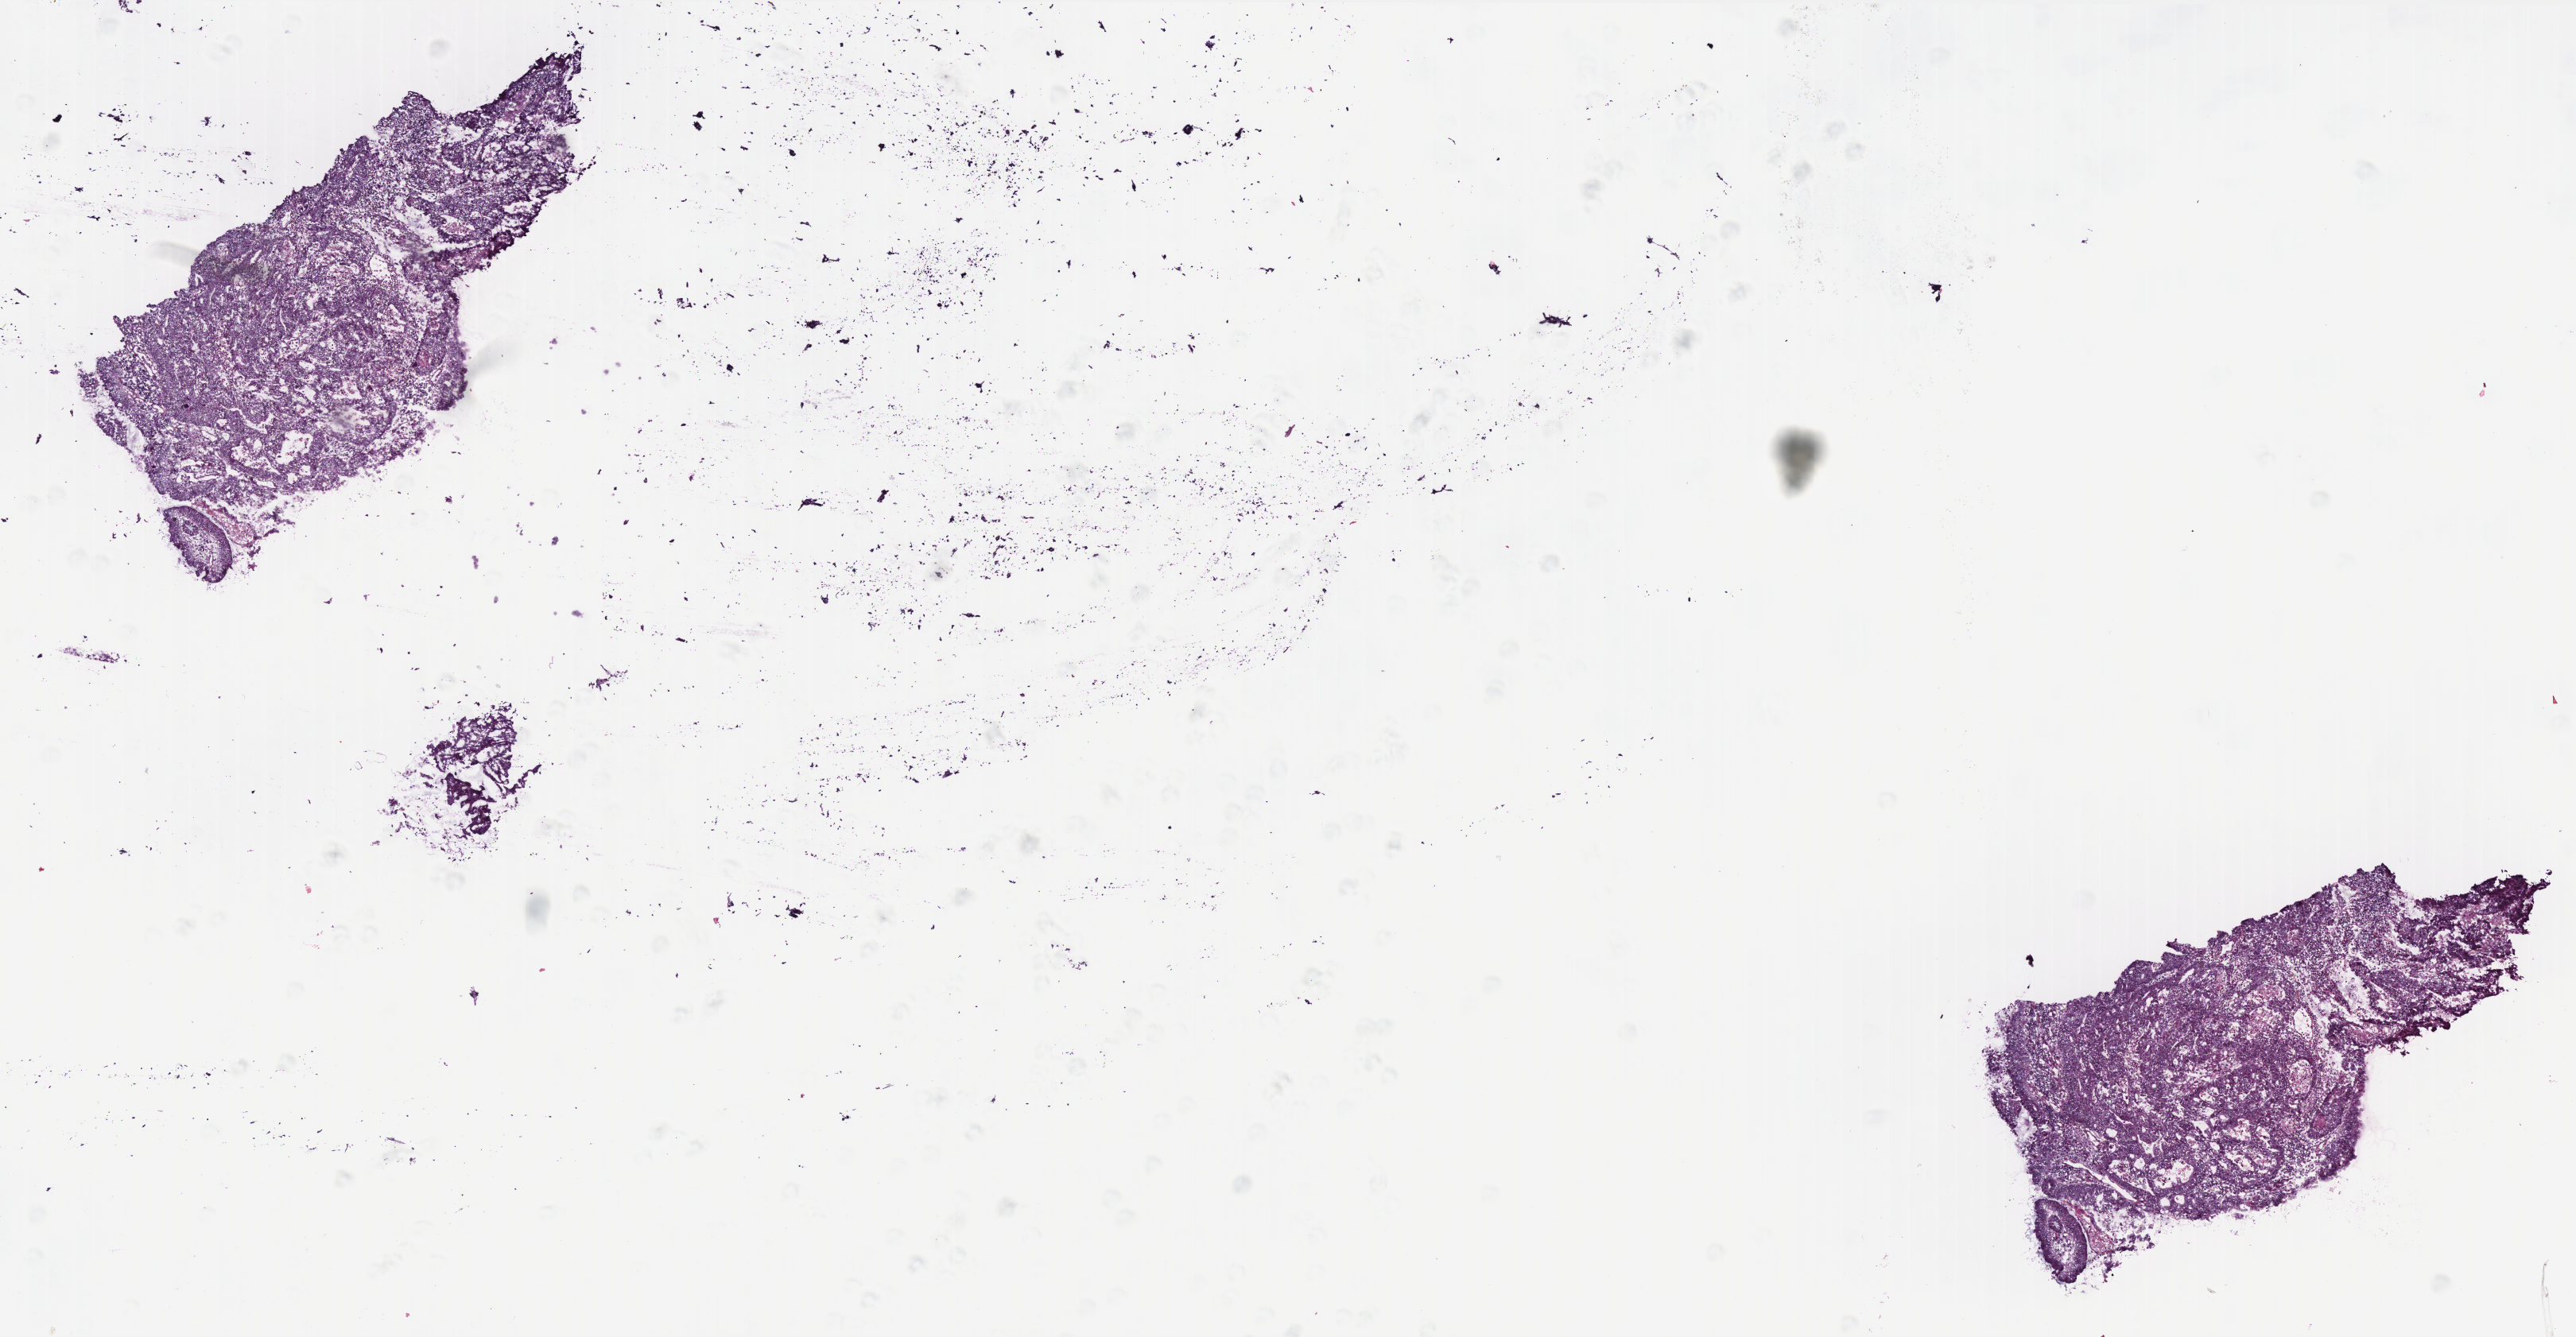
Whole-slide histology image, H&E, whole scanned area (about 13.0 x 6.7 mm, from a 40x scan) shown as a low-resolution overview. Frozen section from the top of the tissue portion. Colon, primary tumour sample. Male patient; age at initial diagnosis 50 years. Pathologist review of this section (percent, as recorded): tumour cells 87%, tumour nuclei 70%, normal cells 0%, stromal cells 8%, necrosis 5%. Infiltration values recorded for this section: lymphocyte infiltration 10%, monocyte infiltration 4%, neutrophil infiltration 10%.
AJCC pathologic stage: IIIB (6th edition). Pathologic diagnosis: Adenocarcinoma, NOS (ascending colon).